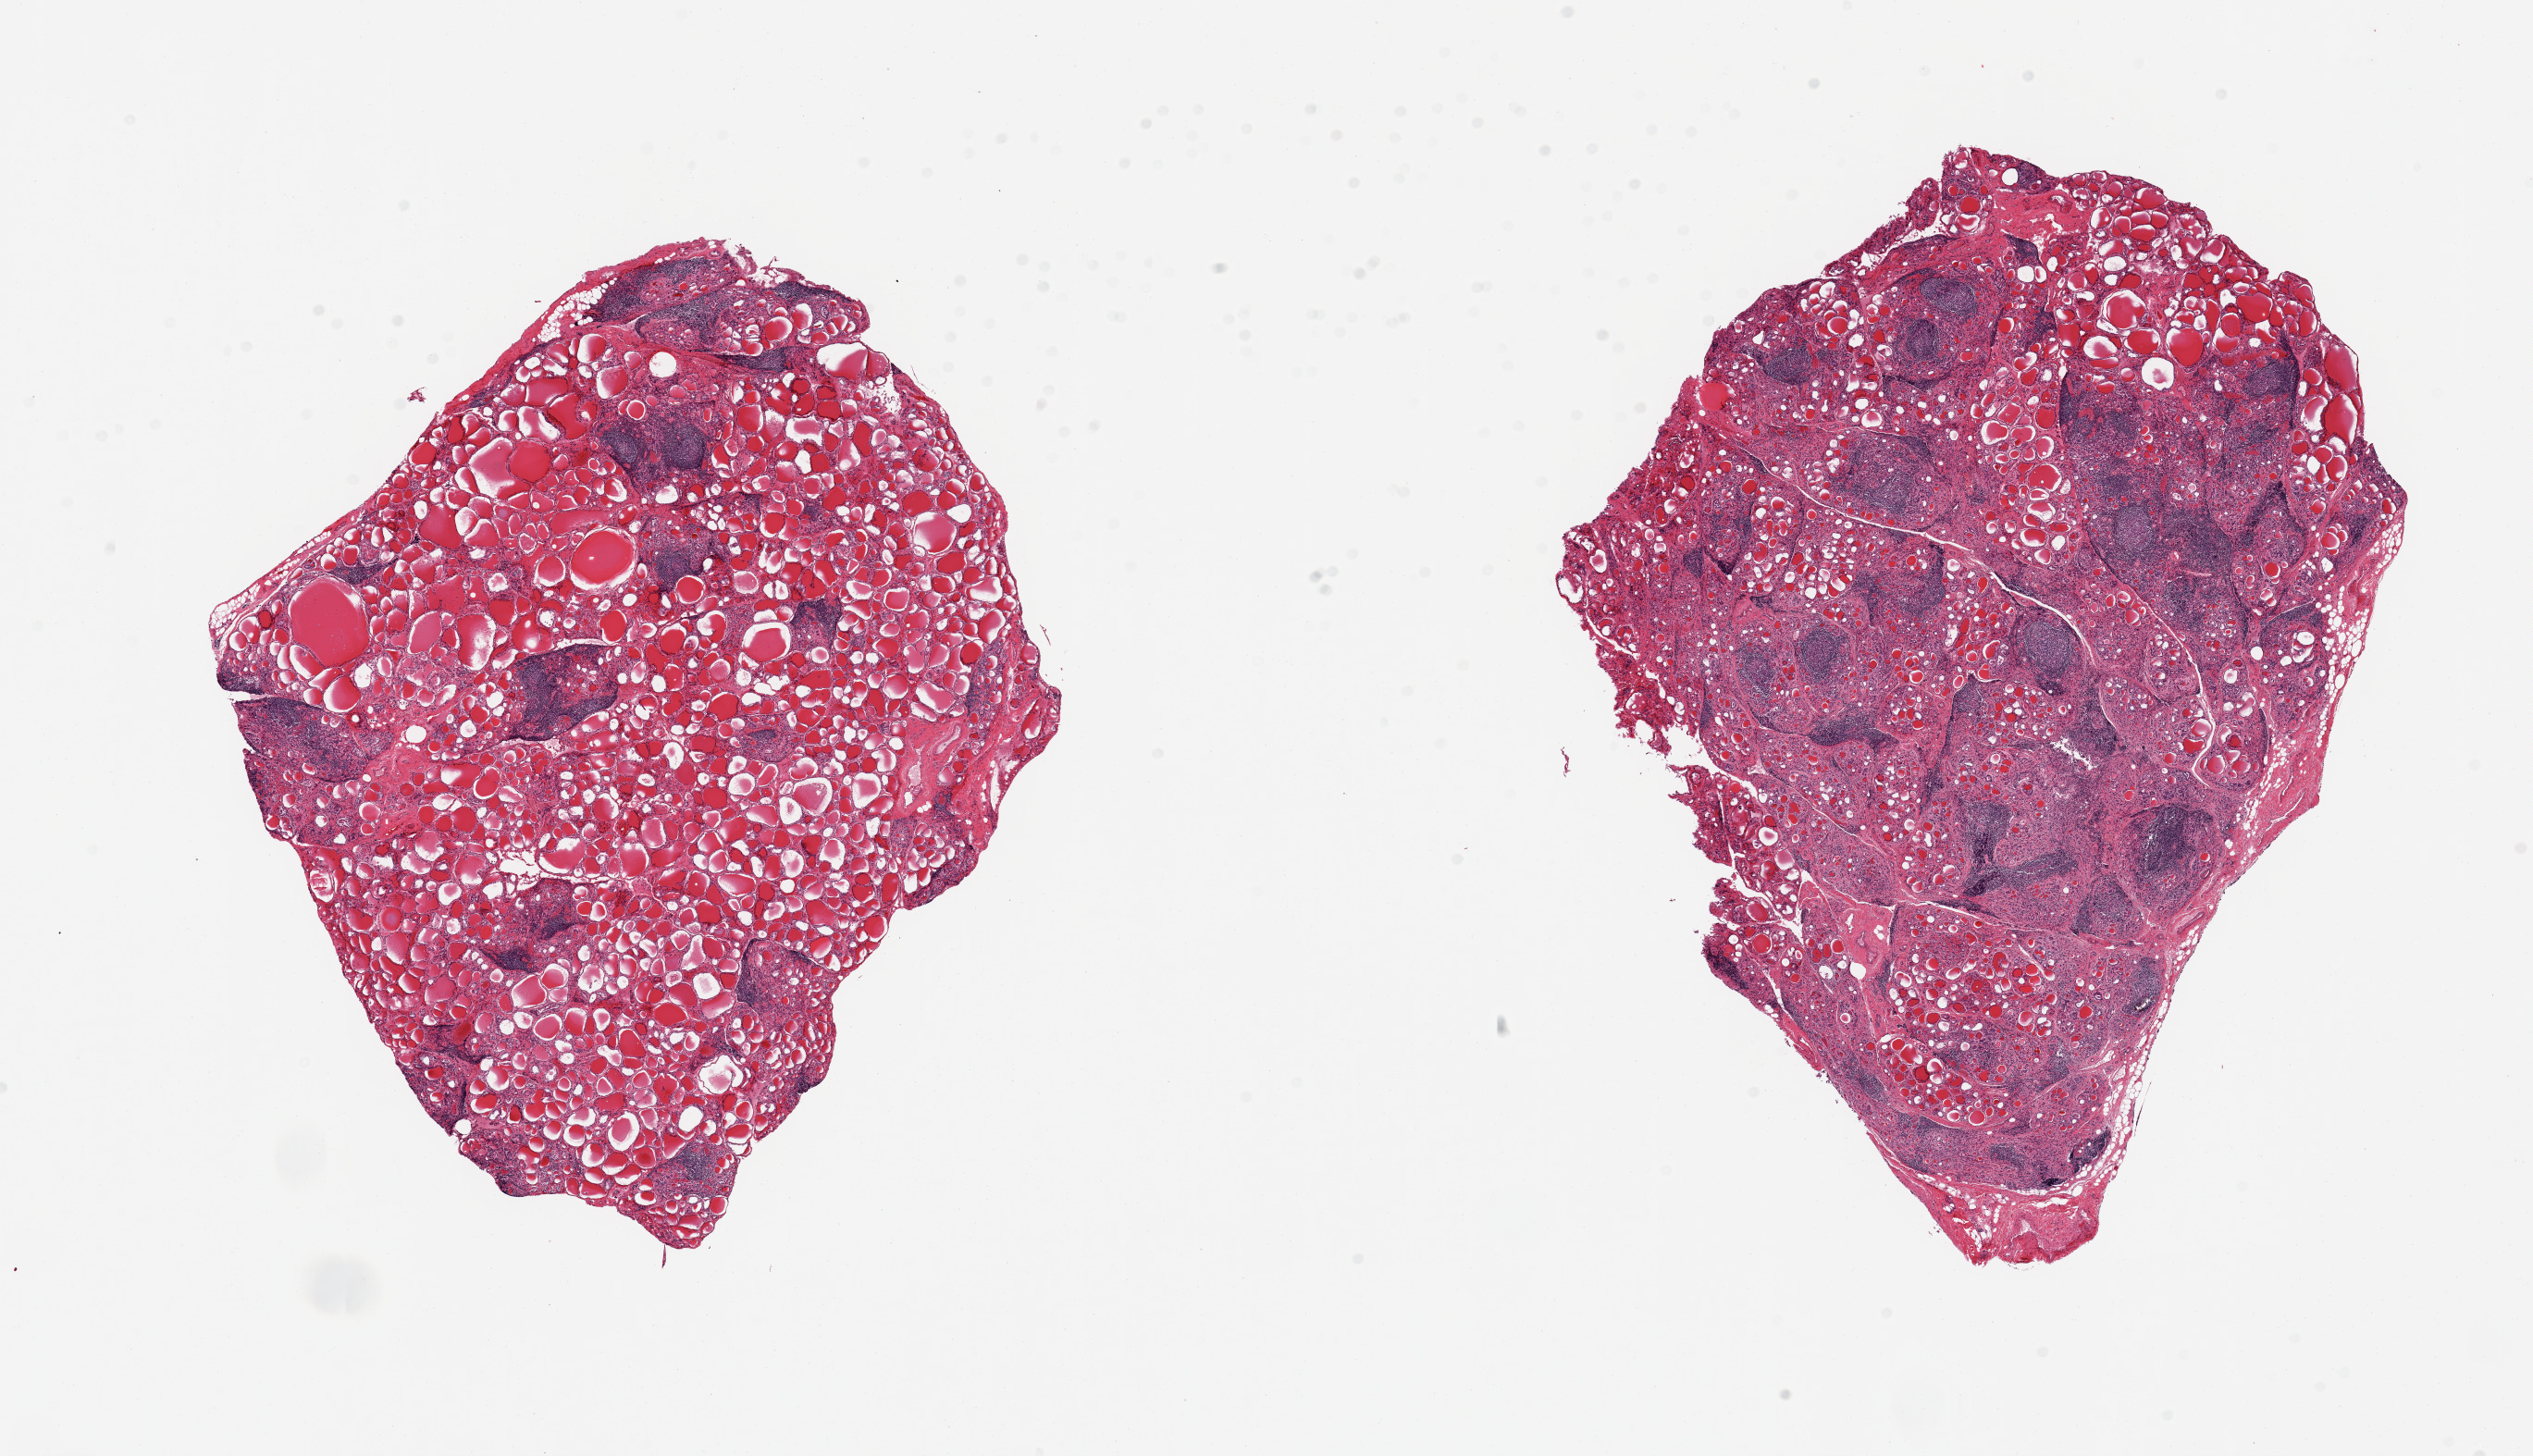
Whole-slide image, haematoxylin and eosin stain — shown as a low-resolution overview of the whole scanned area (about 21.7 x 12.5 mm). PAXgene-fixed, paraffin-embedded tissue. Sampled site (target tissue): thyroid. Donor tissue sample. Donor sex: female.
• review note (as recorded): 2 pieces; moderate lymphocytic (Hashimoto) thyroiditis